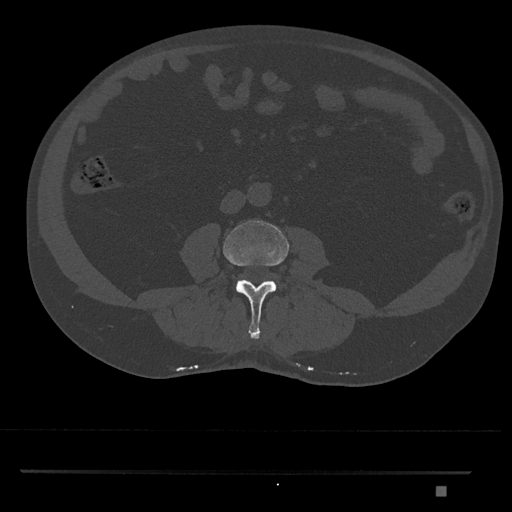
CT including the spine, one axial slice; slice 667 of 1134 in the series (ordered by position); bone window (W 1800 / L 400 HU); 0.5 mm slice thickness; 512 × 512 image matrix, field of view 429 × 429 mm. Male patient, age 65 years. From the clinical record (not read from this slice): primary cancer: prostate.
Outlined on this slice (semi-automatic segmentation, software-assisted and operator-edited):
- L3 vertebra: box from (x=223, y=221) to (x=289, y=340) px